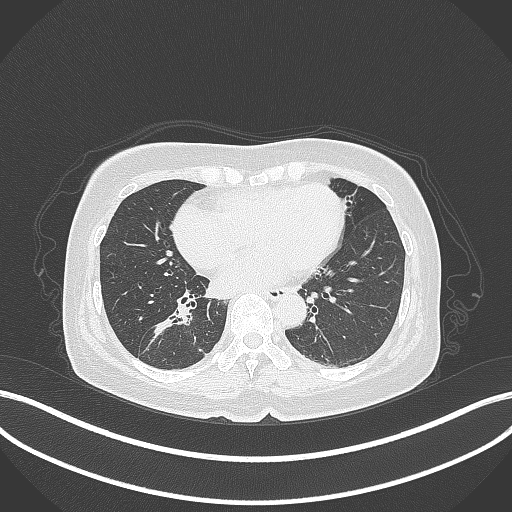
Chest CT, one axial slice; slice 160 of 429 in the series (ordered by position); reconstruction kernel B70f; lung window (W 1500 / L -600 HU); 1 mm slice thickness; 512 × 512 image matrix, field of view 400 × 400 mm. Female patient, age 67 years. From the clinical record (not read from this slice): clinical TNM (as recorded): T1c N1 M0; histopathological grade: G2-3.
Structures marked on this image (bounding box drawn by a radiologist):
- lung tumour (recorded histology: adenocarcinoma): bounding box (x1, y1, x2, y2) in pixels: (136, 300, 193, 361)